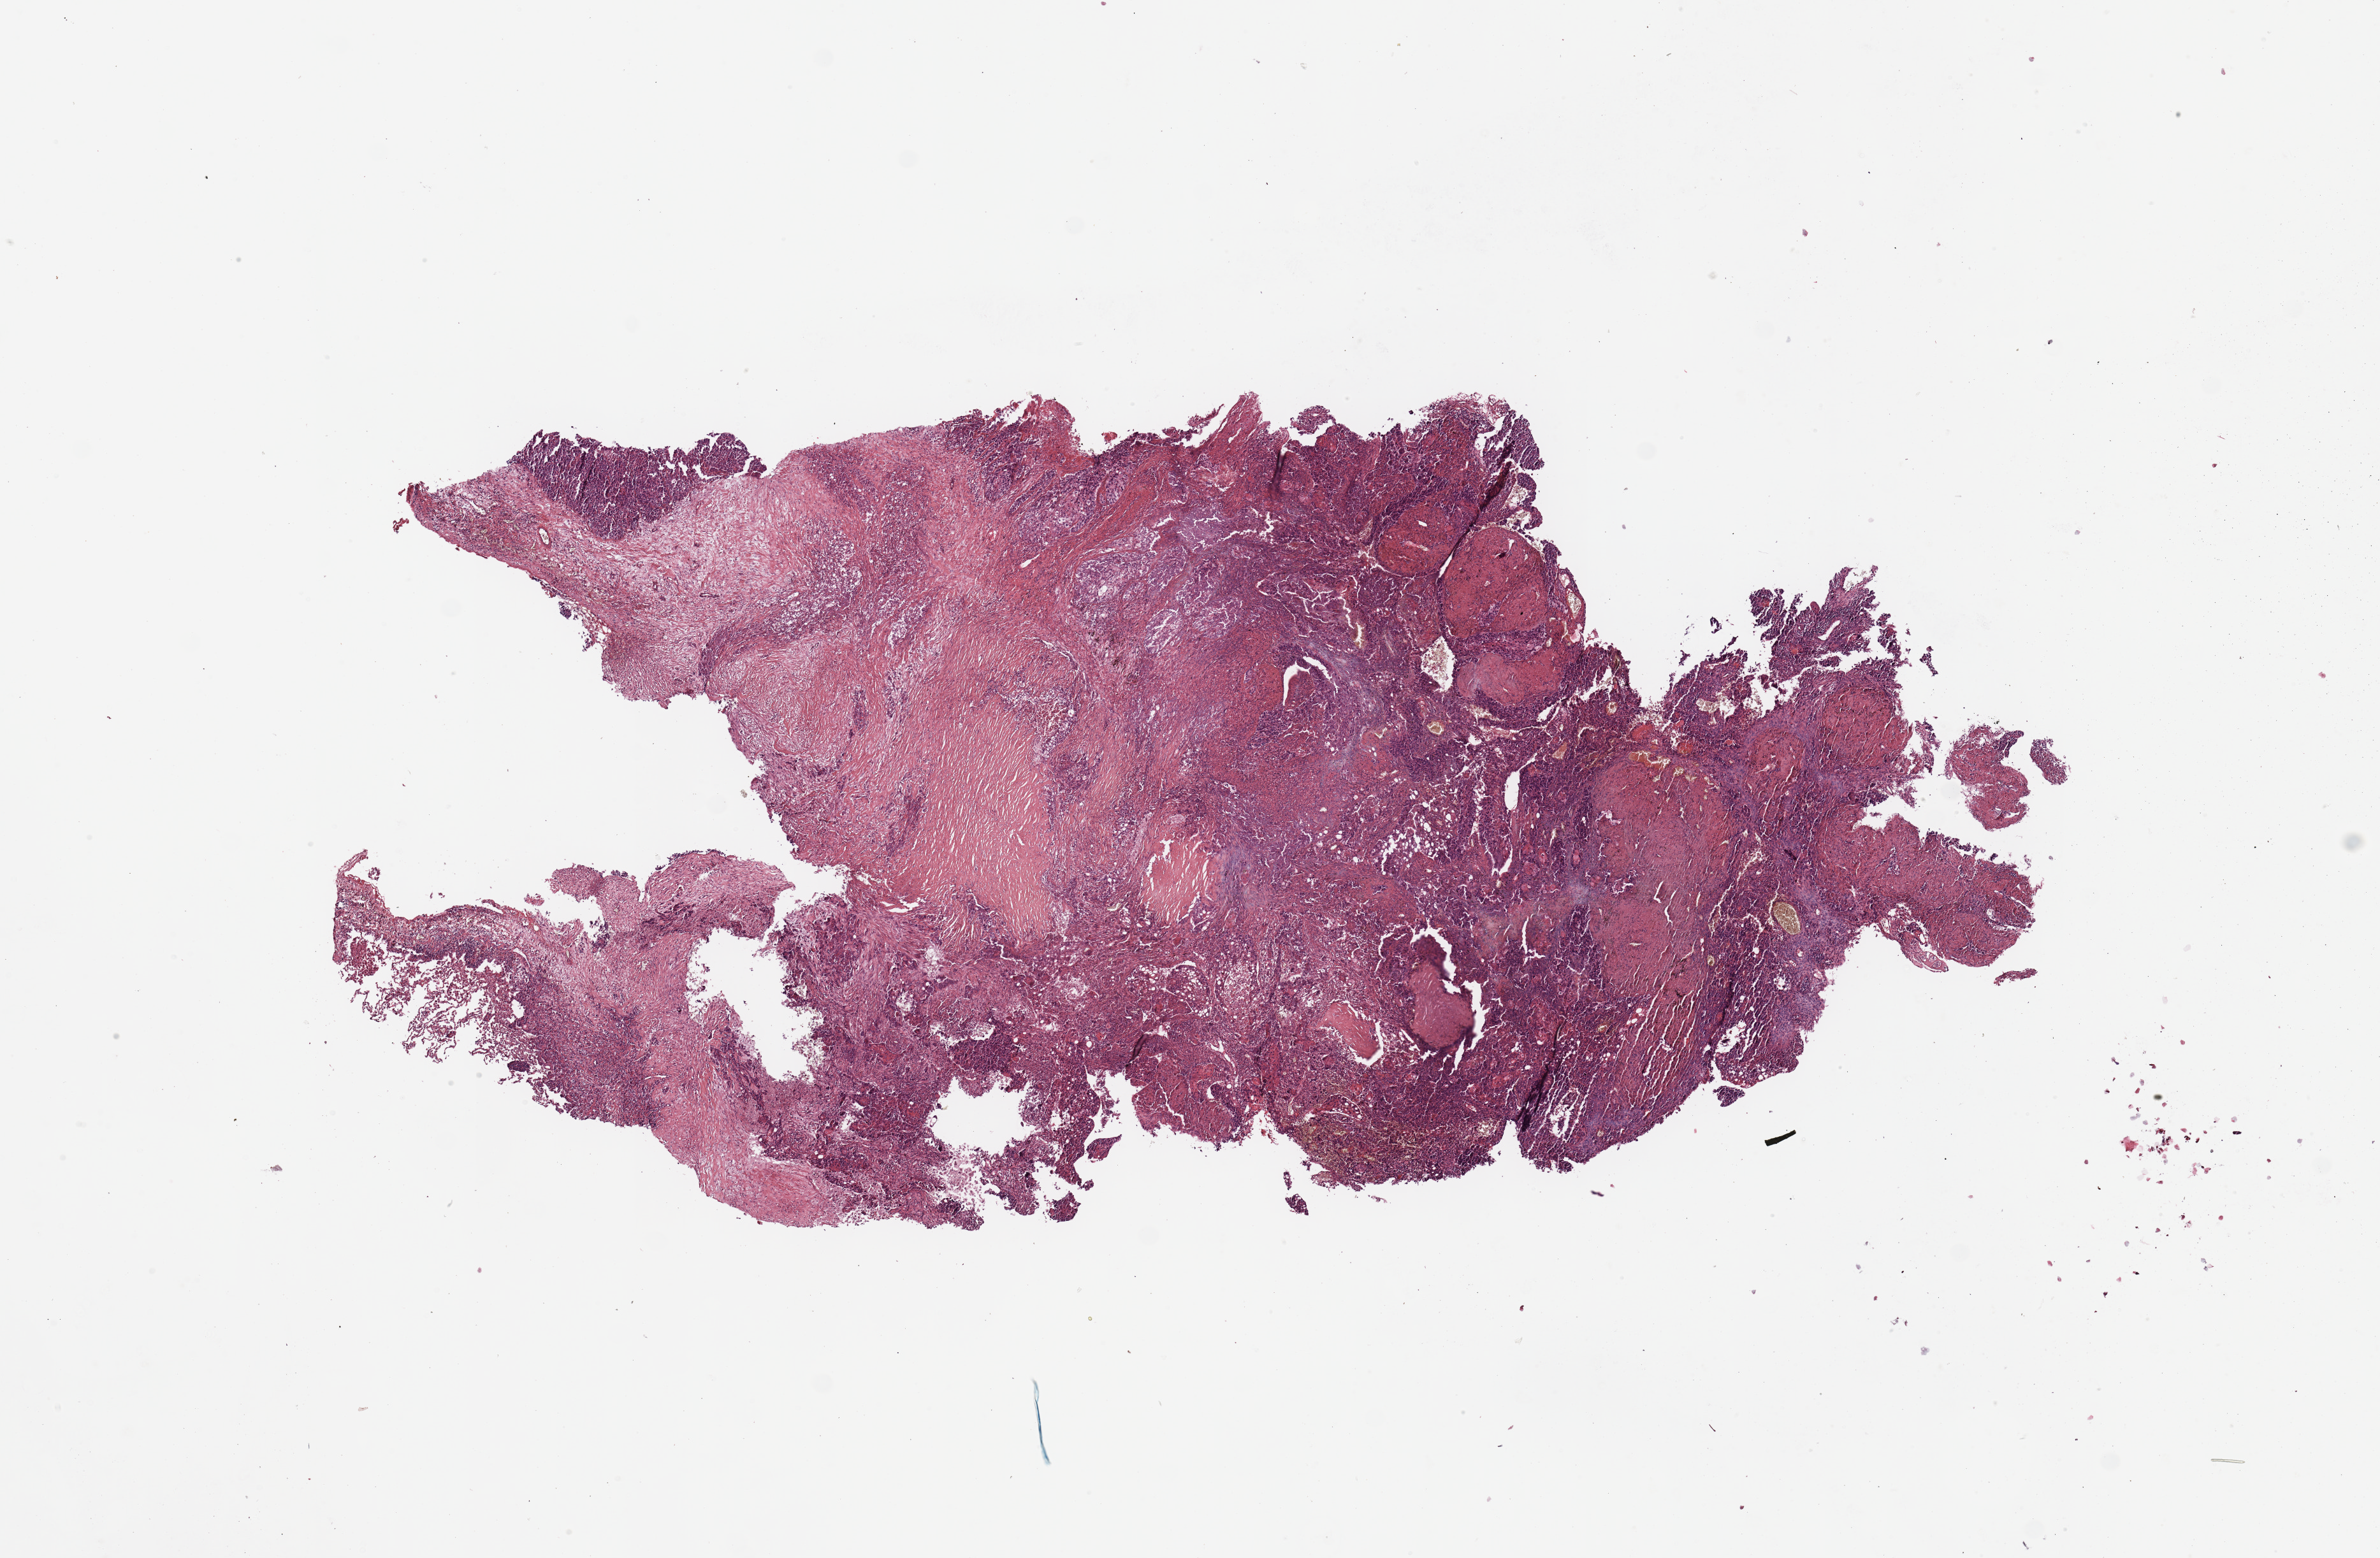
Whole-slide histology image, Hematoxylin and eosin (H&E) stained, shown as a low-resolution overview of the whole scanned area (about 14.8 x 9.7 mm, acquisition: 20x scan); tumour tissue sample, sampled site: lung. Patient: male, age 70 years. Histologic grade: G2 (moderately differentiated). Pathologist review of this section (percent, as recorded): tumour nuclei 70%, necrosis 10%.
Histologic diagnosis: Squamous cell carcinoma, NOS. AJCC pathologic stage: IB. Primary tumour site (as recorded): right middle lobe.